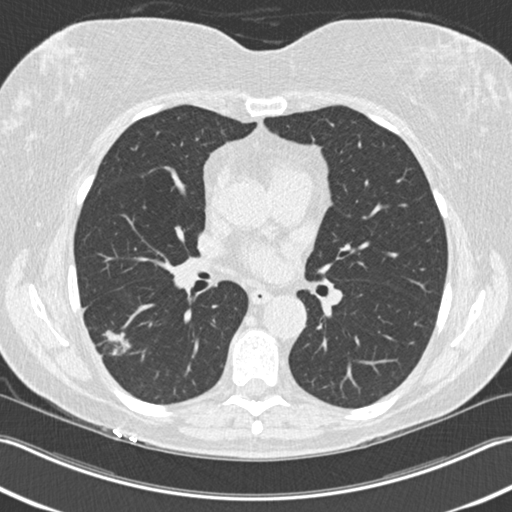
Axial slice from a low-dose chest CT screening exam, baseline annual screen, lung window (W 1500 / L -600 HU), 2 mm slice thickness, standard (soft-tissue) reconstruction kernel (B30f), slice 89 of 211 in the series. Female, age 63 years at enrolment. Current smoker at enrolment.
Expert reader's lesion annotation, box from (x=85, y=320) to (x=144, y=372) px. The screening reader recorded 3 non-calcified nodules or masses ≥4 mm on this exam; which of them this box marks is not recorded. Official screen result: positive, change unspecified: nodule(s) >= 4 mm or enlarging nodule(s), mass(es), or other non-specific abnormalities suspicious for lung cancer. Participant outcome: lung cancer diagnosed 57 days after this screen — bronchiolo-alveolar adenocarcinoma, NOS, right lower lobe, well differentiated (G1), stage IA (AJCC 6th edition), 25 mm at pathology.